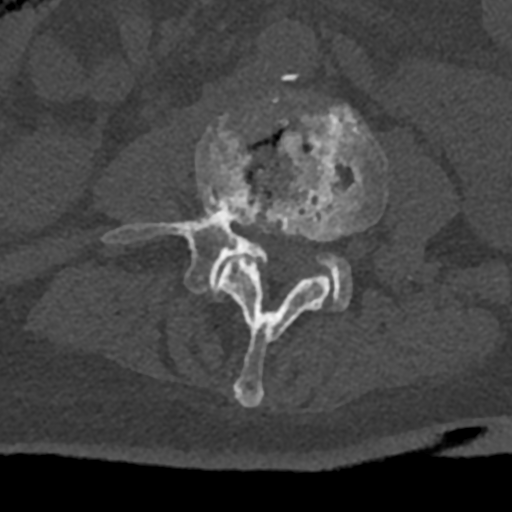
CT including the spine, one axial slice; slice 291 of 797 in the series (ordered by position); bone window (W 1800 / L 400 HU); 512 × 512 image matrix, field of view 160 × 160 mm. Patient: male, 74 years. From the clinical record (not read from this slice): primary cancer: renal.
Outlined on this slice (semi-automatic segmentation, software-assisted and operator-edited):
- L3 vertebra: bounding box [x1, y1, x2, y2] px = [219, 105, 388, 407]
- L4 vertebra: [103, 113, 351, 310]